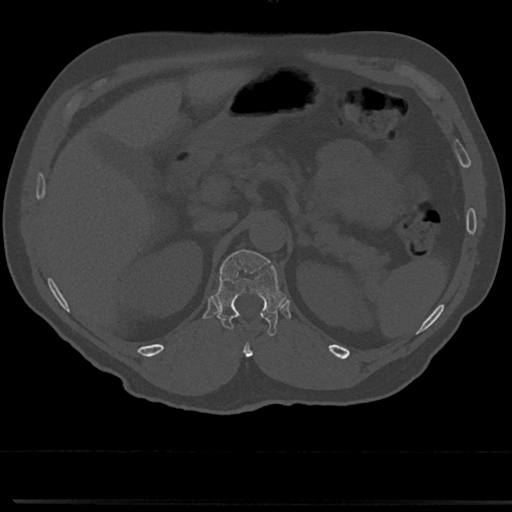
CT including the spine, one axial slice. Position 156 of 817 along the scan axis. Bone window (W 1800 / L 400 HU). 0.5 mm slice thickness. 512 × 512 image matrix, field of view 355 × 355 mm. Patient: male, 61 years. From the clinical record (not read from this slice): primary cancer: prostate.
Structures marked on this image (semi-automatically segmented with operator editing):
- T12 vertebra: bounding box (x1, y1, x2, y2) in pixels: (216, 248, 282, 334)